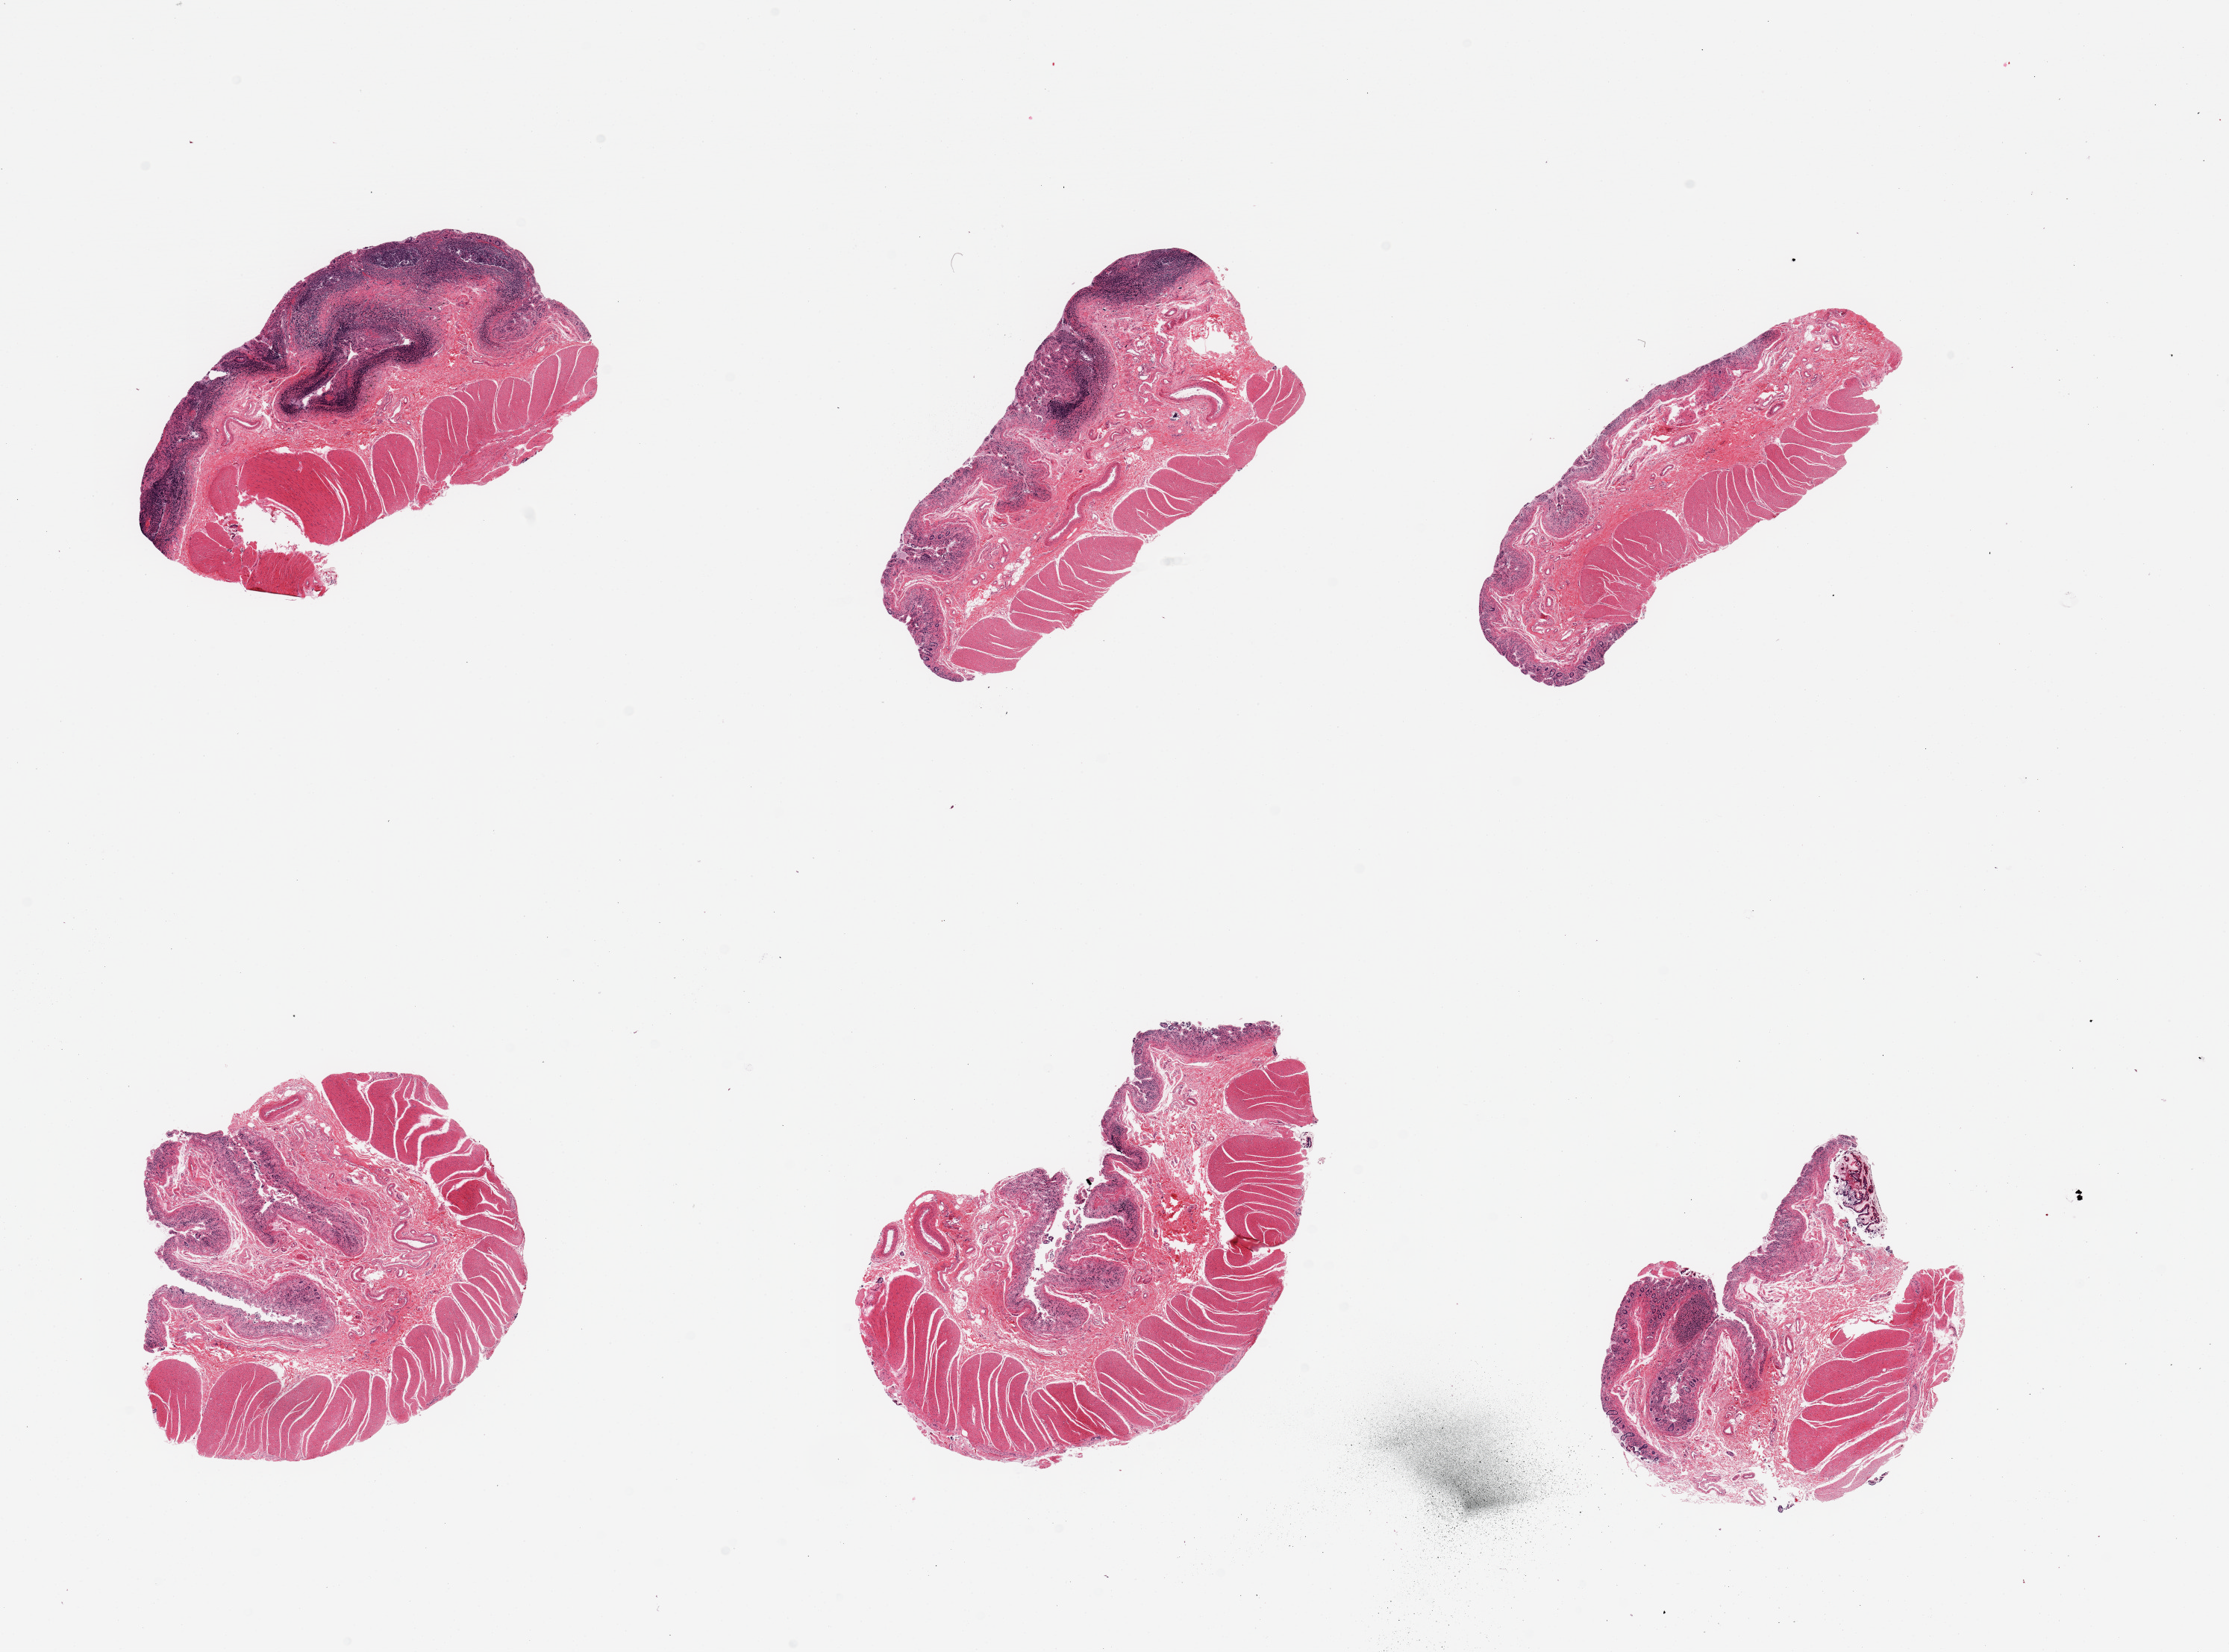
Haematoxylin and eosin whole-slide image, brightfield — whole scanned area (about 23.6 x 17.5 mm) shown as a low-resolution overview. PAXgene-fixed, paraffin-embedded tissue. Target tissue: ileum. Tissue donor sample. Donor sex: male.
Pathologist's review note for this sample: 6 pieces; several lymphoid nodules in 3 pieces; all have muscularis propria (not target).